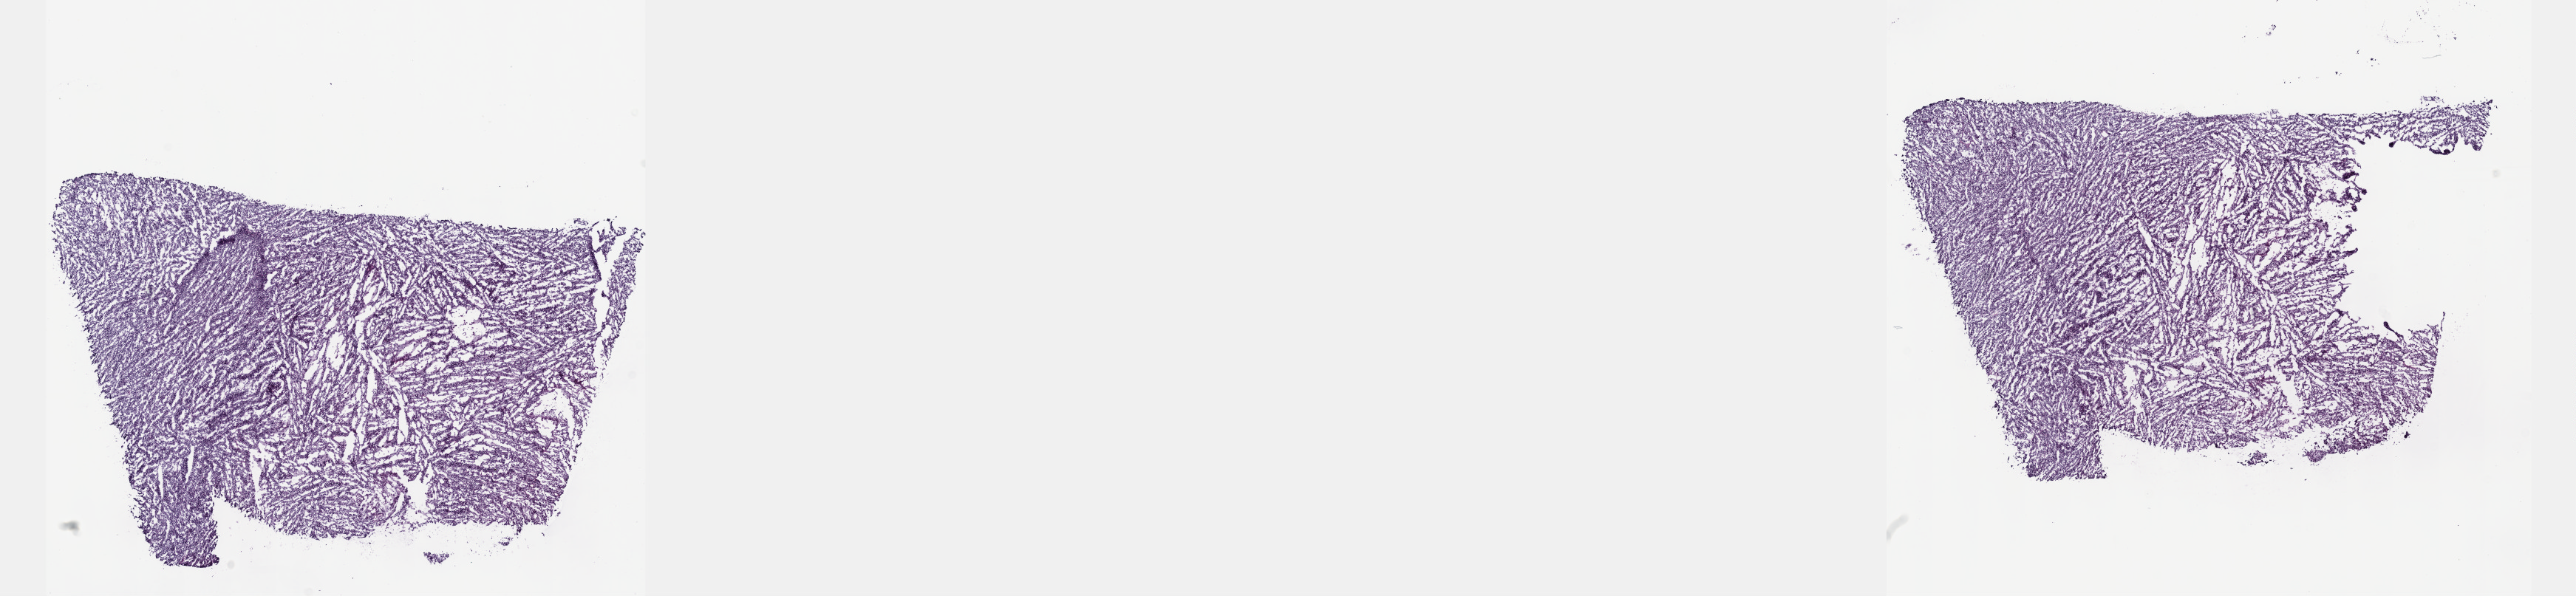
Hematoxylin and eosin (H&E) stained whole-slide image, whole scanned area (about 28.2 x 6.5 mm) shown as a low-resolution overview. Frozen section. Sample: primary tumour, kidney. Female, age 66 years at initial diagnosis. Composition of this section per pathologist review: tumour cells 88%, tumour nuclei 95%, normal cells 0%, stromal cells 5%, necrosis 7%. Inflammatory infiltration, as recorded: lymphocyte infiltration 2%, monocyte infiltration 1%, neutrophil infiltration 1%.
Laterality: right. AJCC pathologic stage: I. Pathologic diagnosis: Papillary adenocarcinoma, NOS.